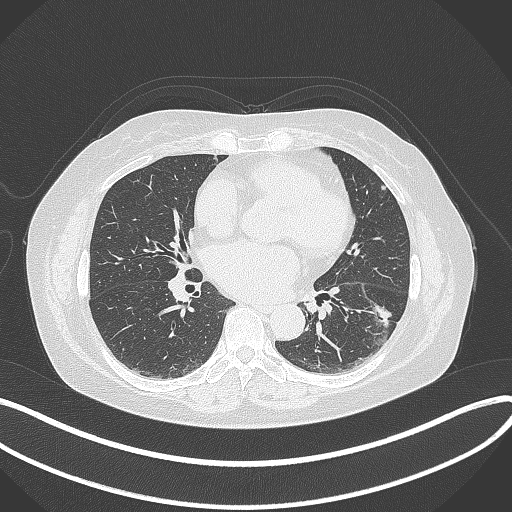
Chest CT, one axial slice. Position 168 of 373 along the scan axis. Reconstruction kernel B70f. Lung window (W 1500 / L -600 HU). 1 mm slice thickness. 512 × 512 image matrix, field of view 400 × 400 mm. Patient: female, 67 years. From the clinical record (not read from this slice): clinical TNM (as recorded): T1c N0 M0; histopathological grade: G2.
Outlined on this slice (bounding box drawn by a radiologist):
- lung tumour (recorded histology: adenocarcinoma): bounding box [x1, y1, x2, y2] px = [362, 296, 397, 354]